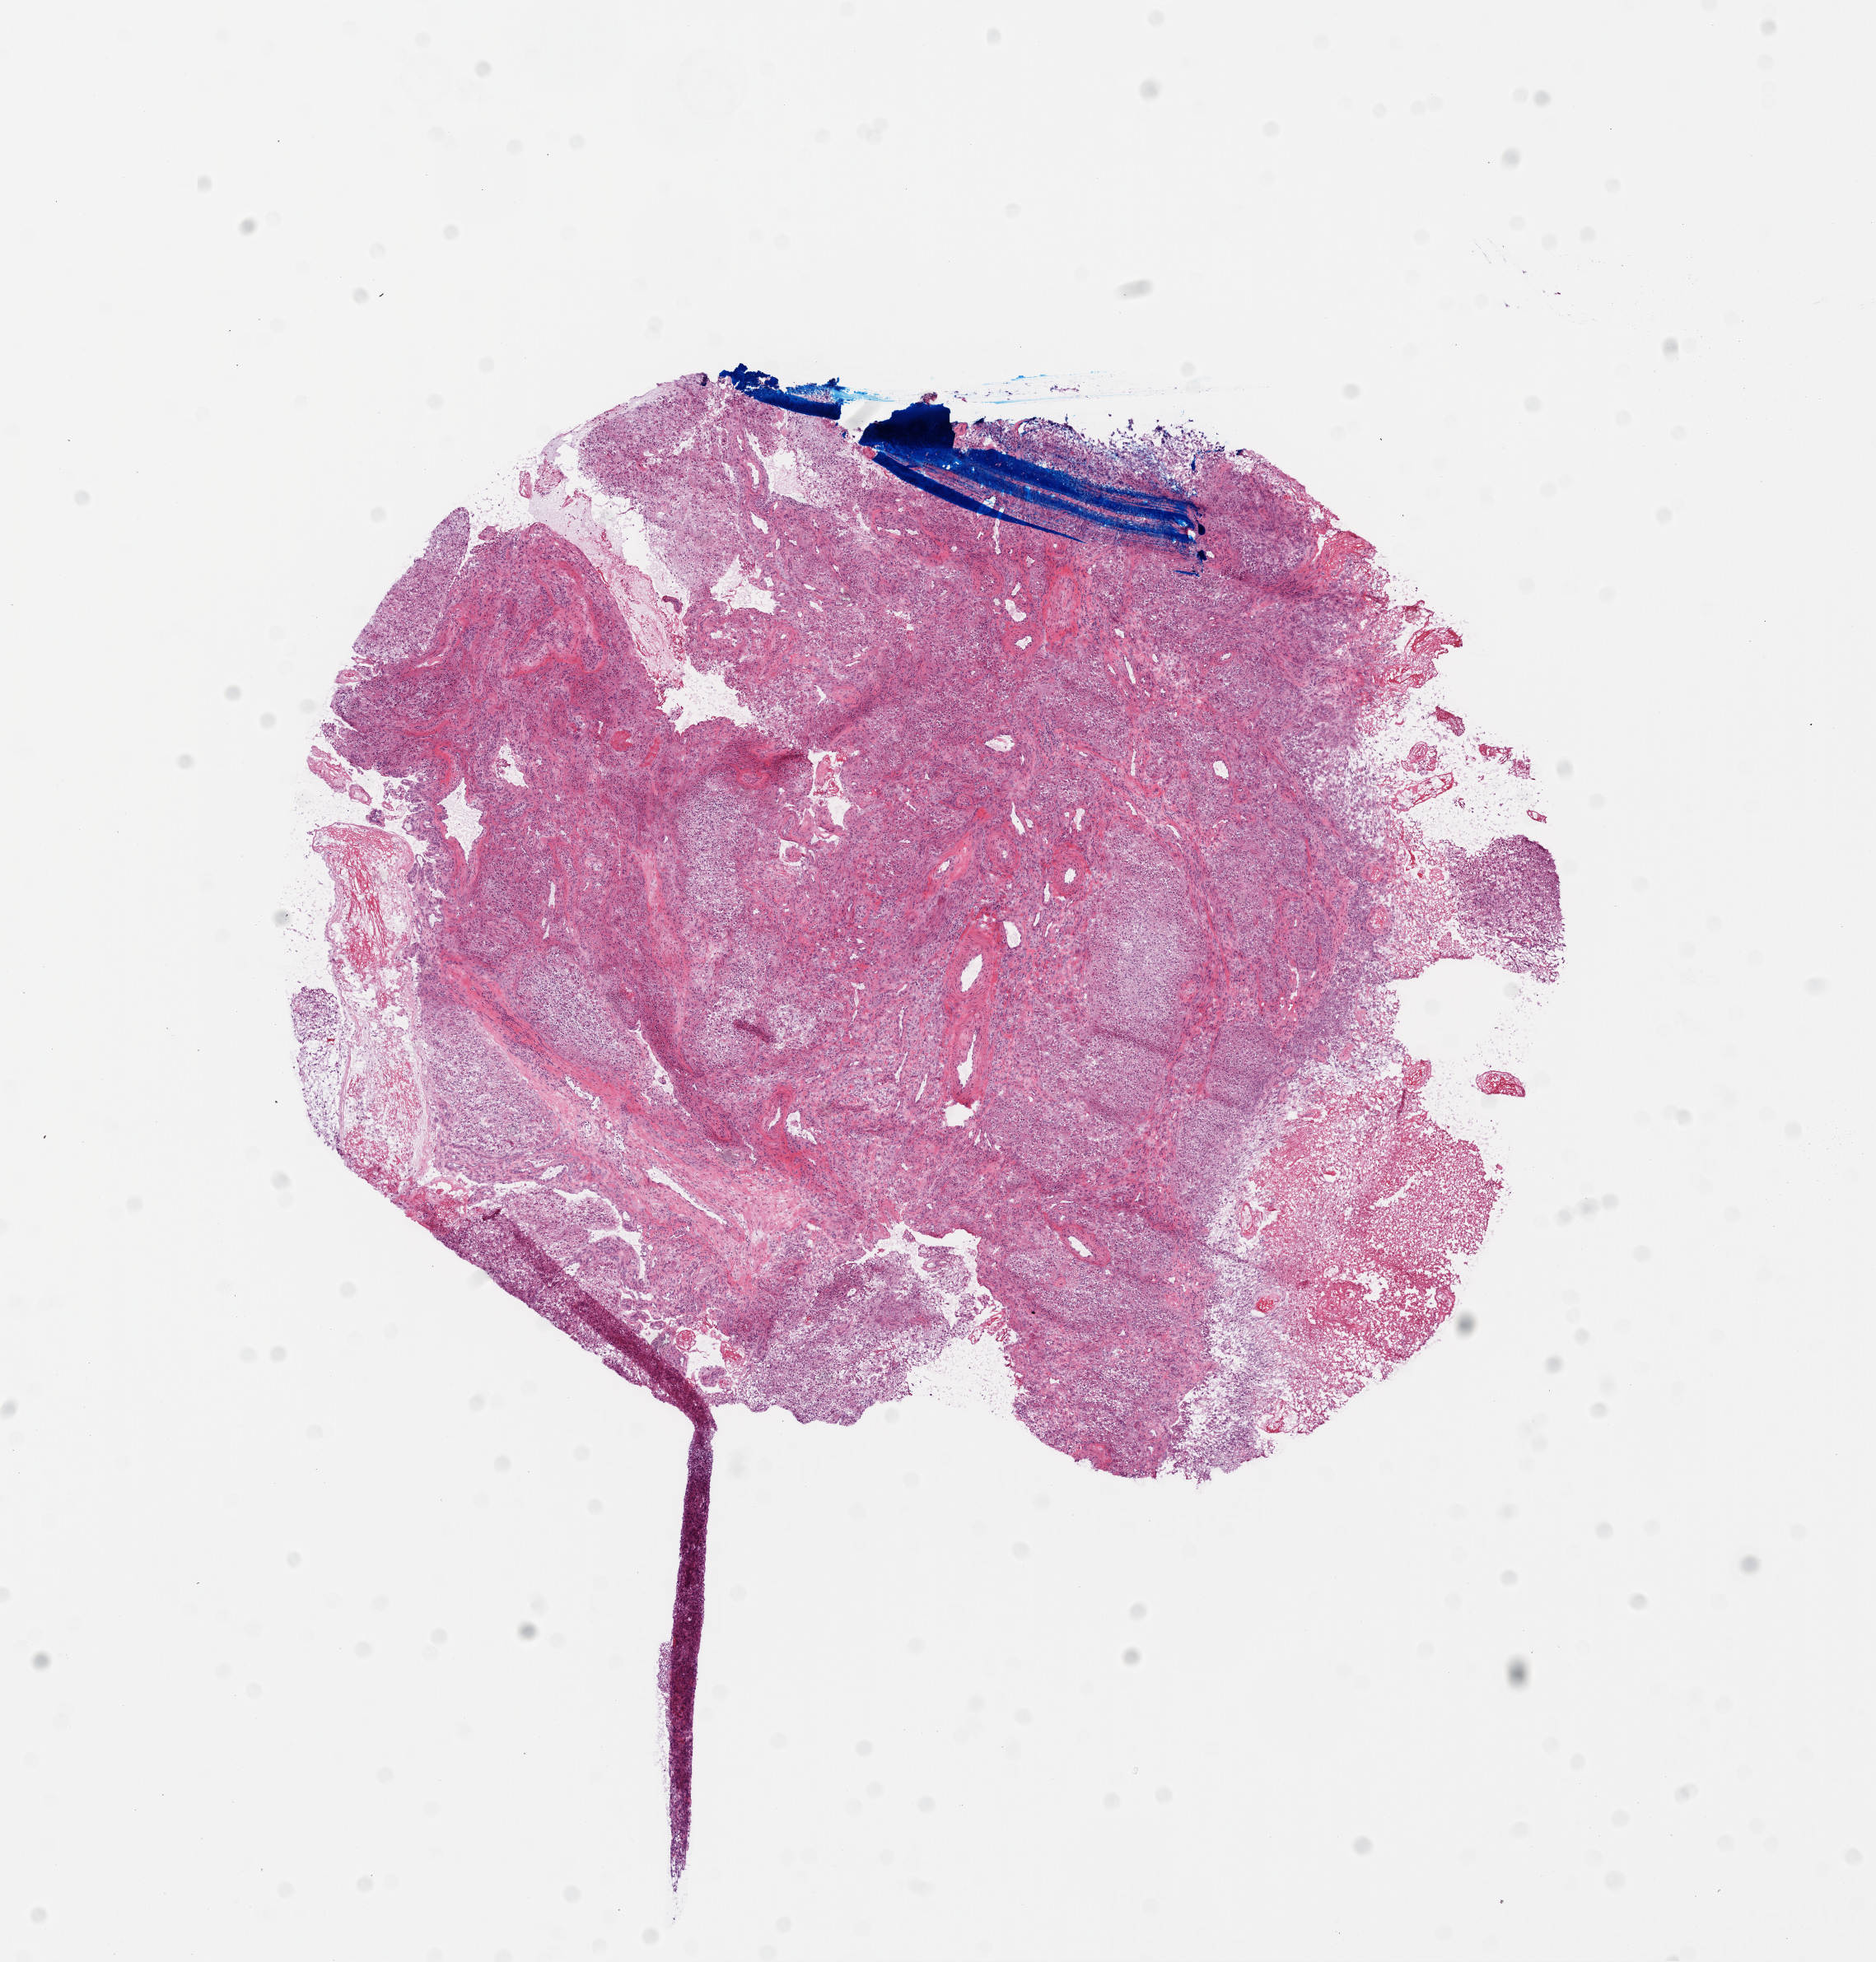
Whole-slide histology image, Hematoxylin and eosin (H&E) stained — shown as a low-resolution overview of the whole scanned area (about 9.2 x 9.6 mm, from a 20x scan); frozen section from the top of the tissue portion; brain, primary tumour sample. Male, age 43 years at initial diagnosis. Slide review estimates, as recorded: tumour cells 80%, tumour nuclei 90%, normal cells 0%, stromal cells 10%, necrosis 10%.
Histologic diagnosis: Glioblastoma.